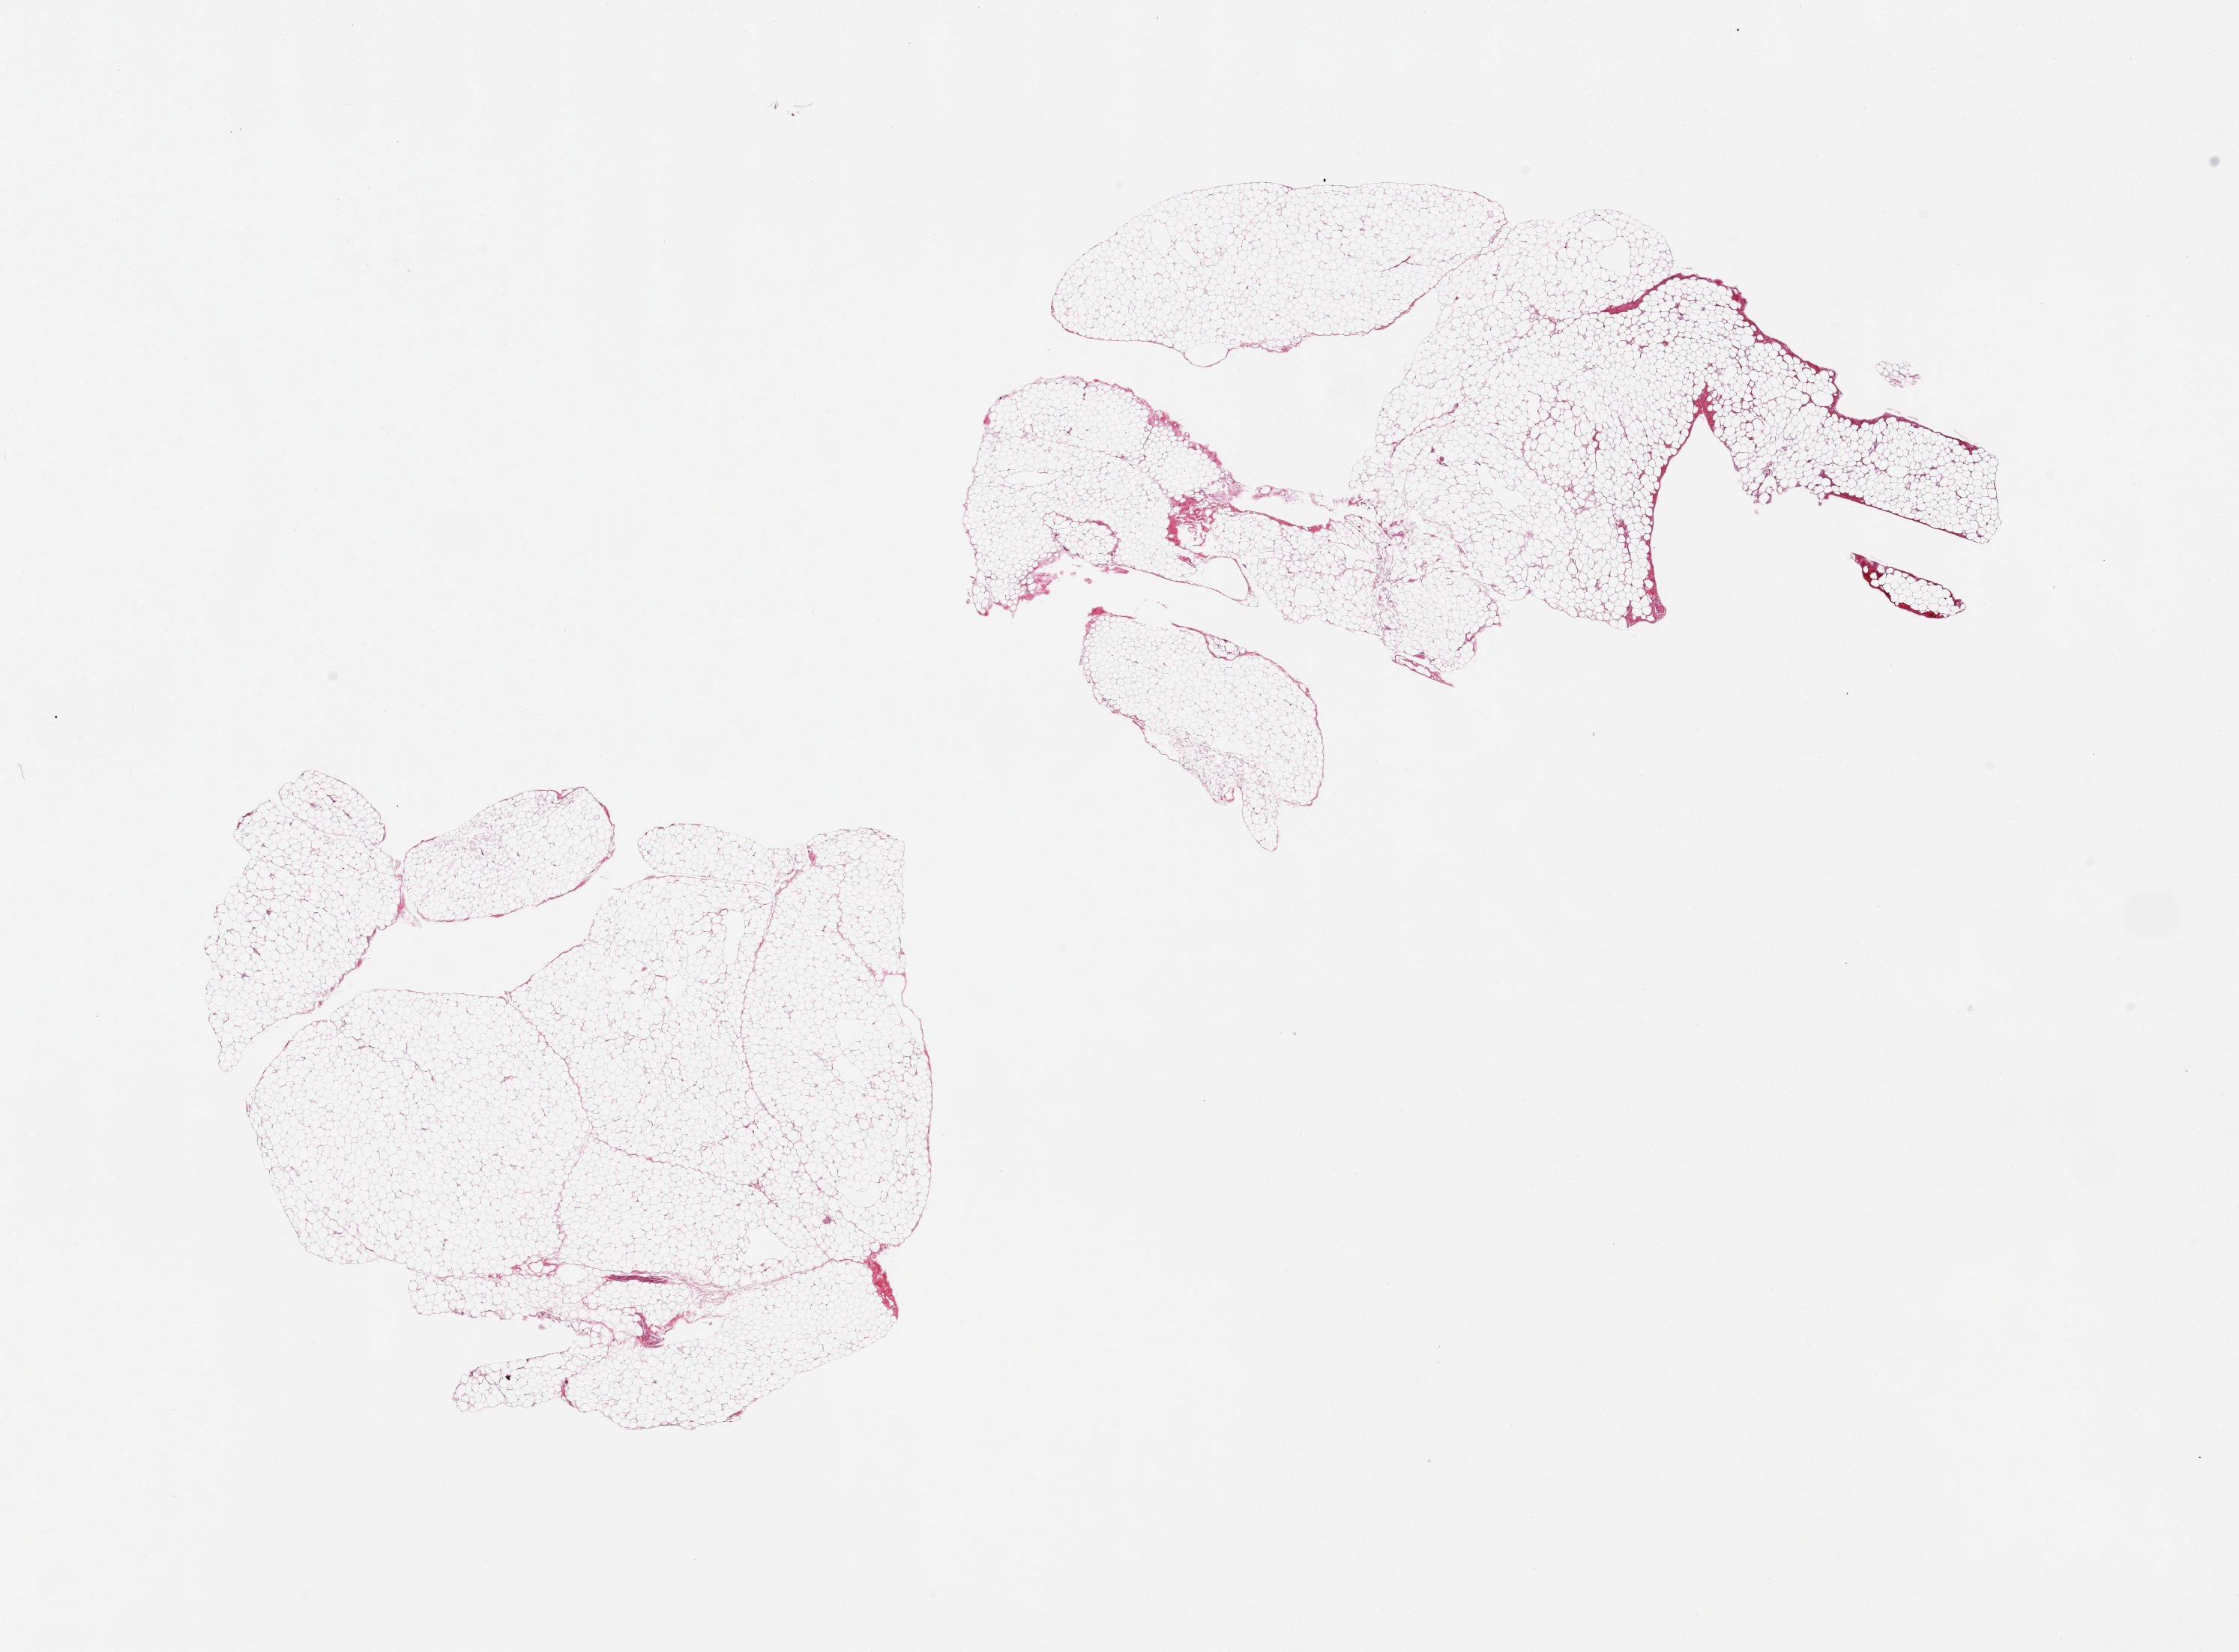
Digitized hematoxylin and eosin (H&E)-stained section, low-resolution overview of the scanned area, about 23.6 x 17.4 mm, PAXgene-fixed, paraffin-embedded tissue, sampled site (target tissue): omentum, tissue donor sample. Donor sex: female.
• pathologist's review note for this sample: 2 pieces, minimal 'contaminant' vessel/fibrous tissue